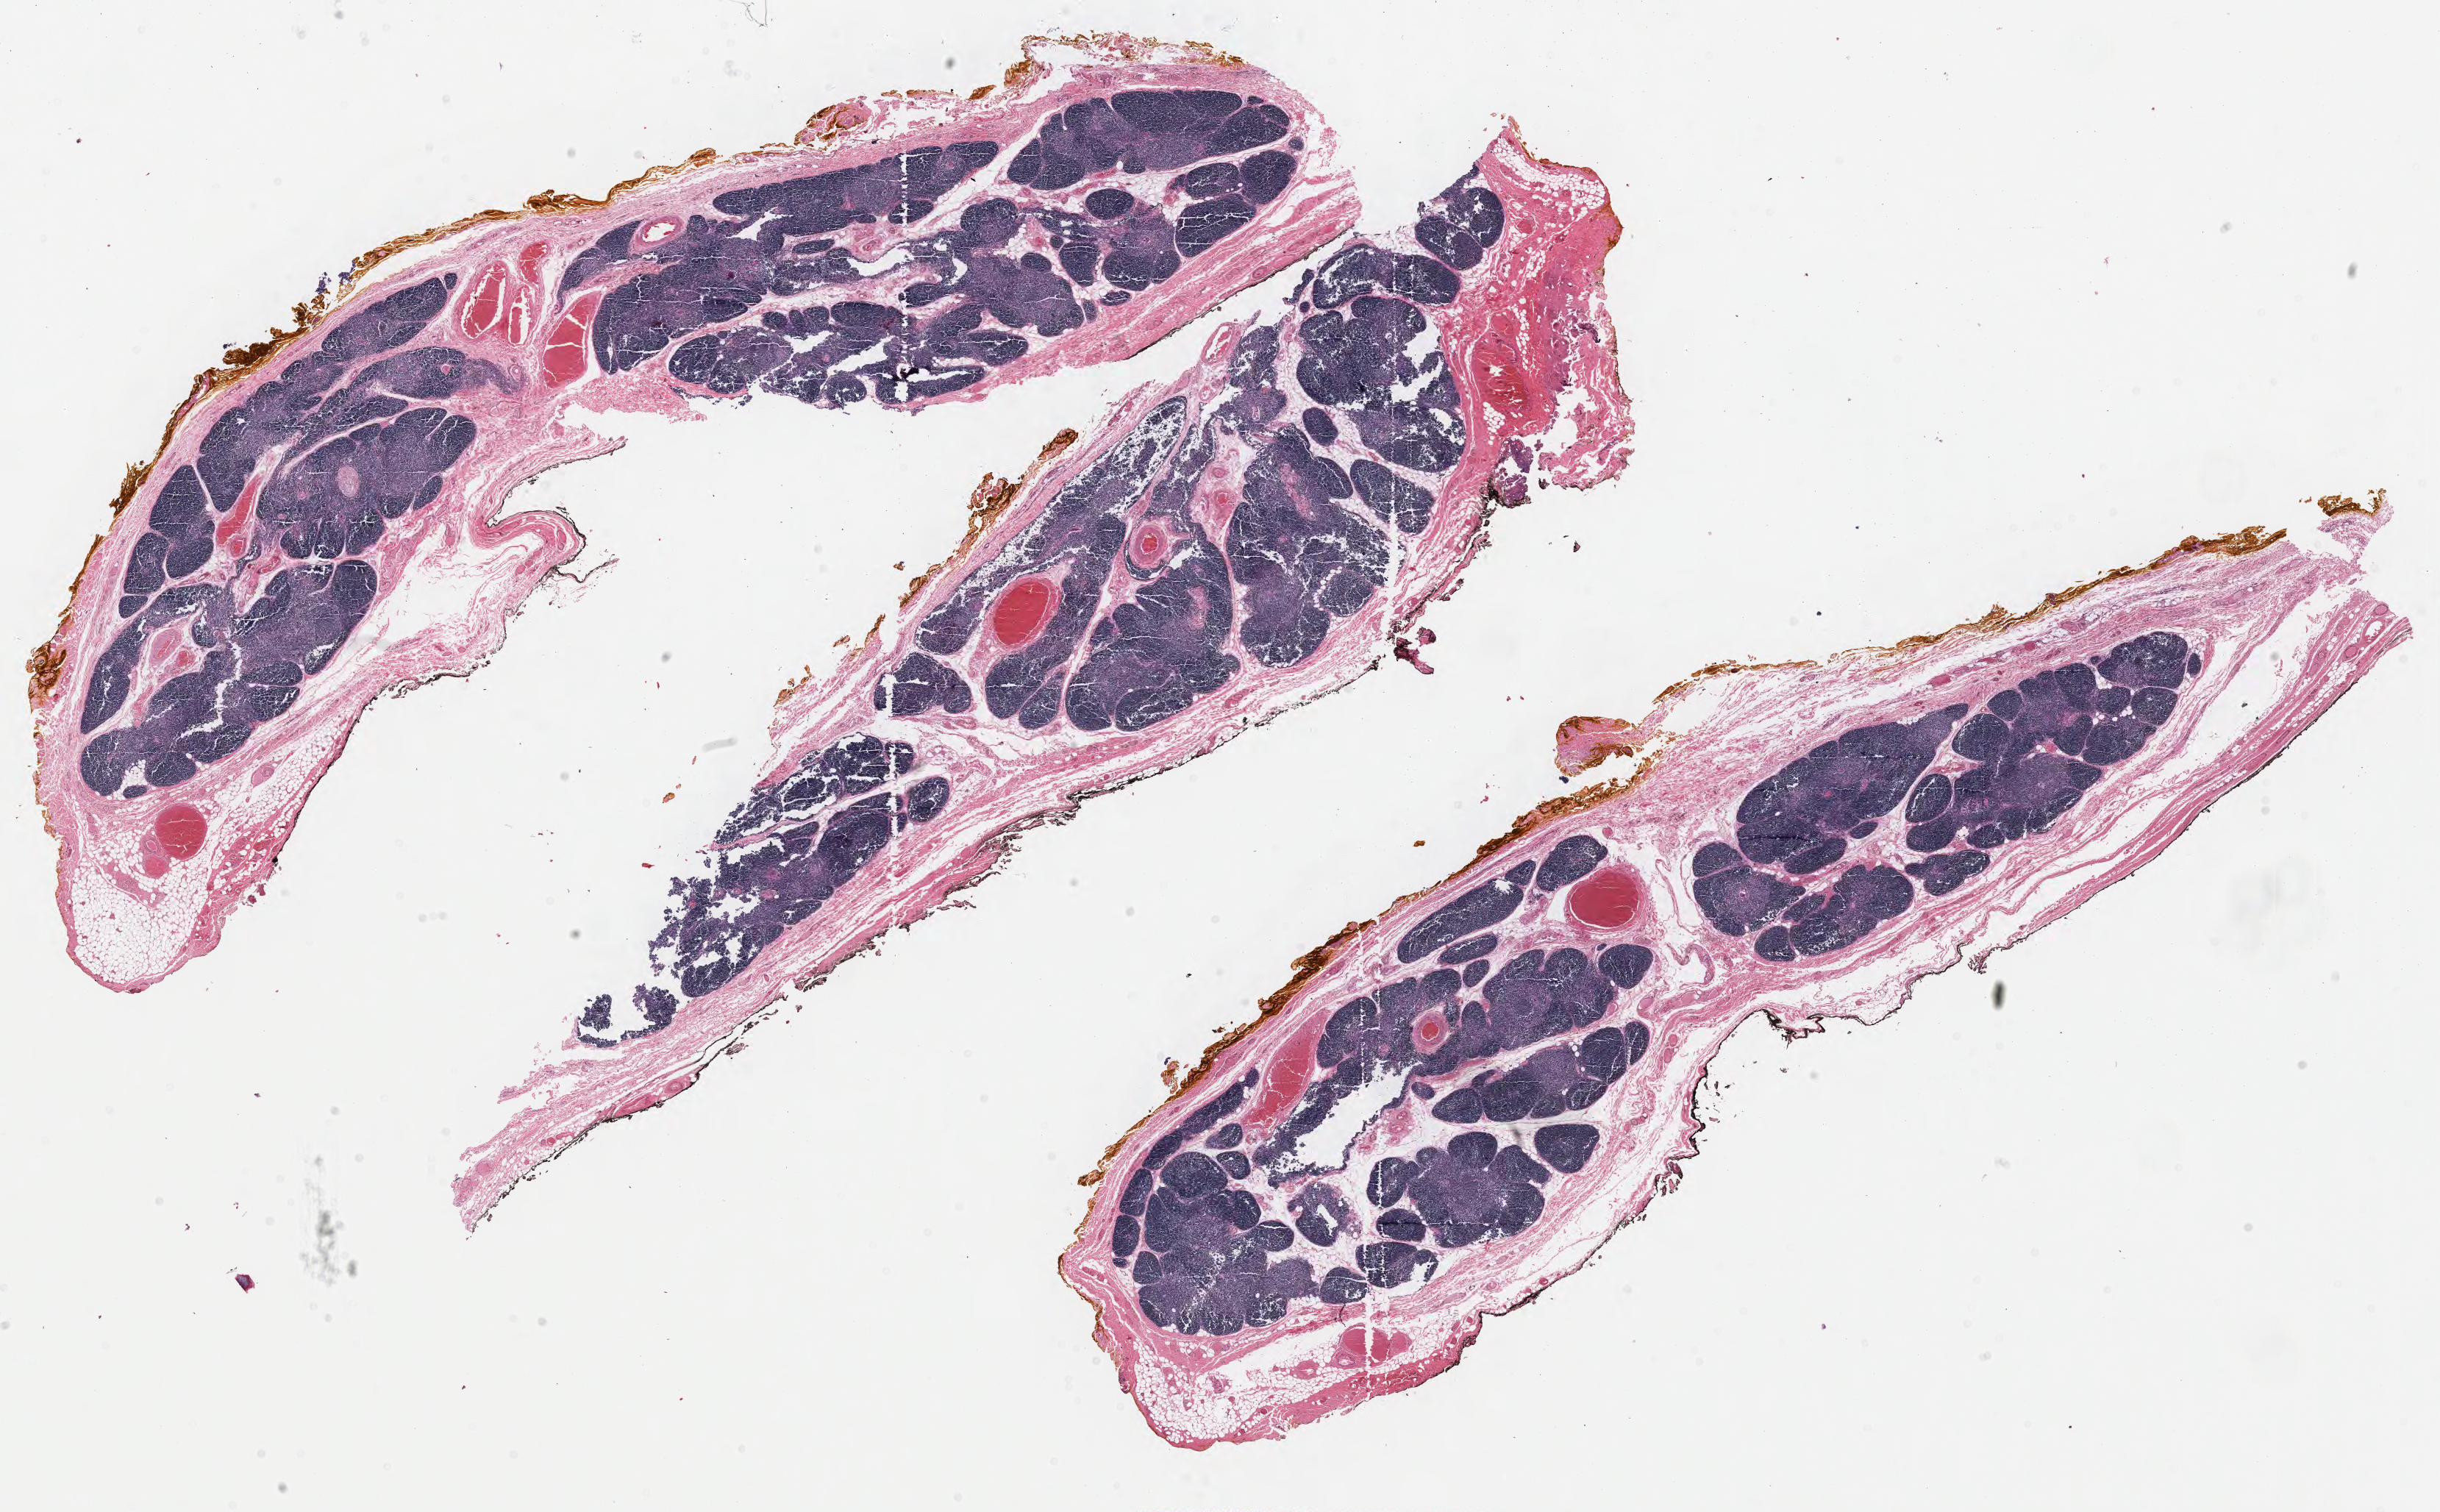
Digitized H&E tissue section (whole slide), shown as a low-resolution overview of the whole scanned area (about 26.3 x 16.3 mm); formalin-fixed paraffin-embedded (FFPE) diagnostic section; primary tumour sample from the thymus. Patient: female, age at initial diagnosis 57 years.
- histologic diagnosis: Thymoma, type B1, NOS